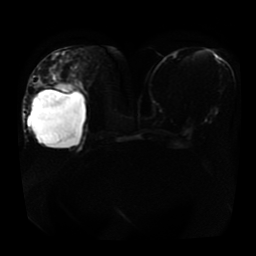
Breast MRI, one axial slice. Position 20 of 41 along the scan axis. Diffusion-weighted series; image 2 of 4 stored at this slice position (different b-values; order by instance number). 1.5 T. 5 mm slice thickness. 256 × 256 image matrix, field of view 360 × 360 mm. Female patient.
Annotated regions visible in this slice (outlined manually by an expert reader):
- tumour on diffusion-weighted imaging: bounding box (x1, y1, x2, y2) in pixels: (56, 86, 74, 93)